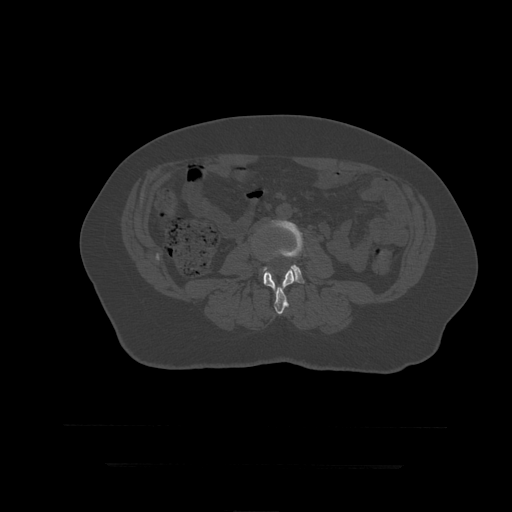
CT including the spine, one axial slice; position 112 of 399 along the scan axis; reconstruction kernel STANDARD; 120 kVp; bone window (W 1800 / L 400 HU); 512 × 512 image matrix. Patient age 41 years. From the clinical record (not read from this slice): primary cancer: breast.
Outlined on this slice (semi-automatic segmentation, software-assisted and operator-edited):
- L3 vertebra: bounding box [x1, y1, x2, y2] px = [263, 268, 298, 315]
- L4 vertebra: [263, 220, 305, 284]